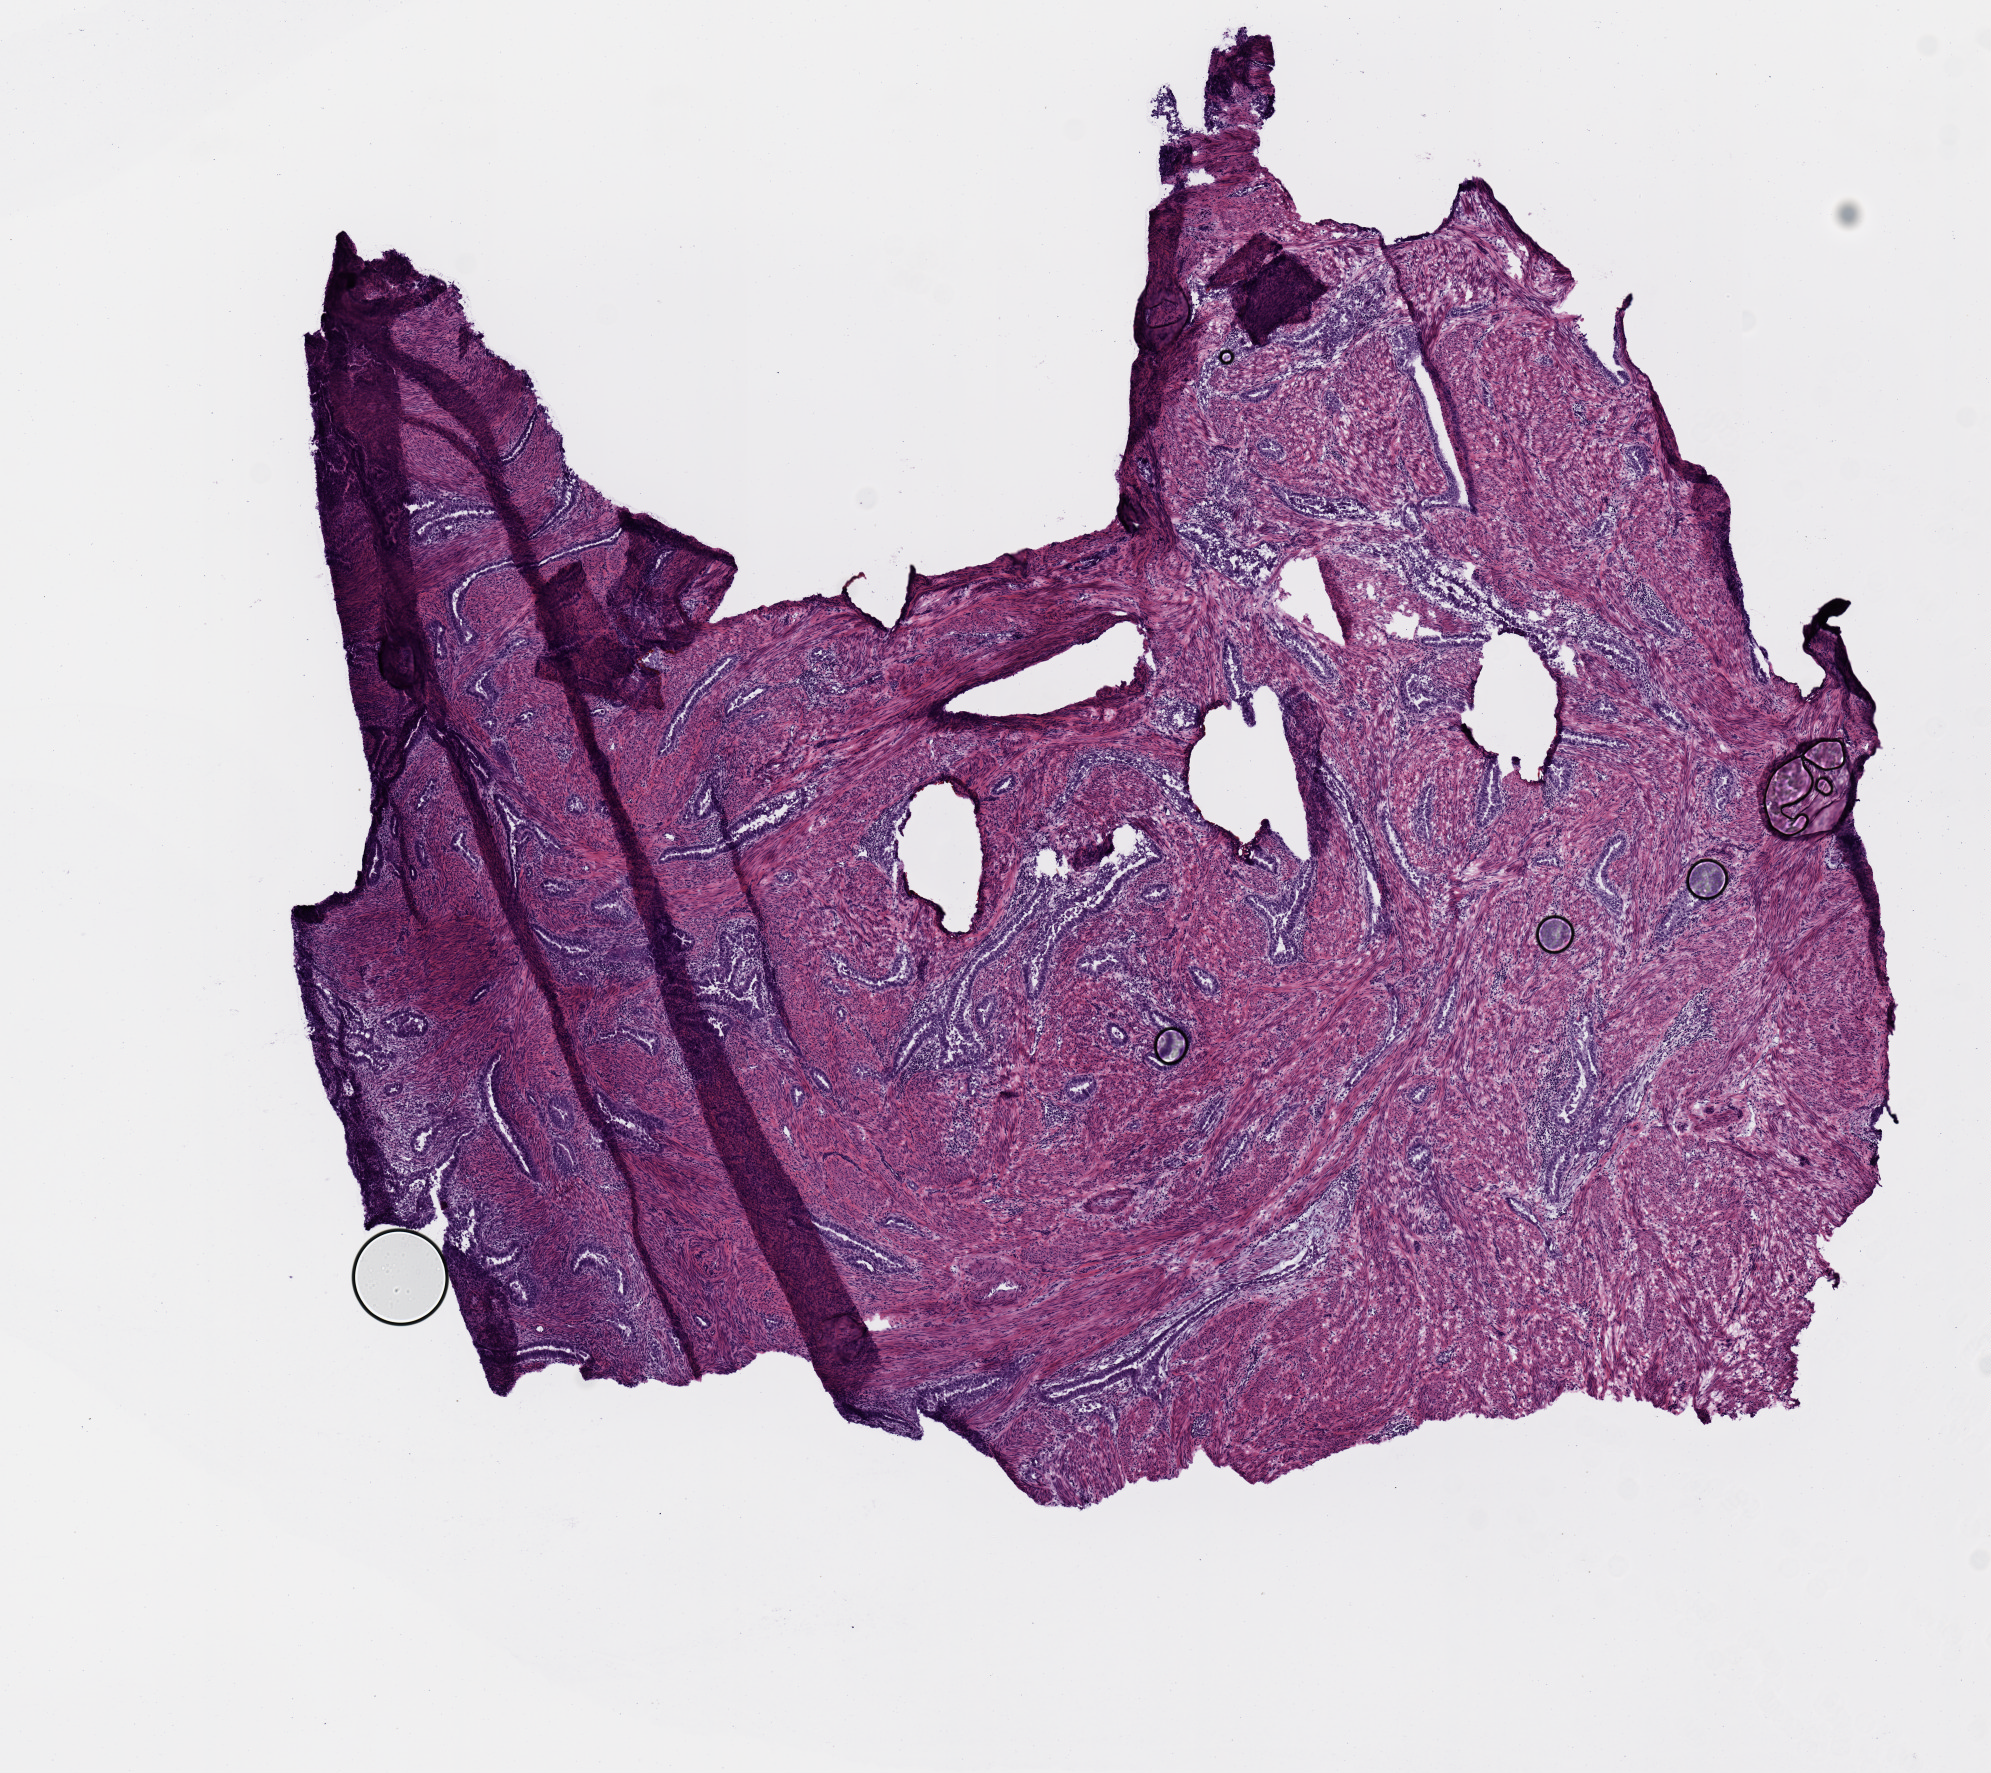
Whole-slide histology image, H&E-stained — shown as a low-resolution overview of the whole scanned area (about 7.9 x 7.0 mm, slide scanned at 20x); frozen section; primary tumour sample from the uterus. Female, age 60 years at initial diagnosis. Histologic grade: G3 (poorly differentiated). Slide review estimates, as recorded: tumour cells 80%, tumour nuclei 60%, normal cells 0%, stromal cells 20%, necrosis 0%. Infiltration values recorded for this section: lymphocyte infiltration 0%, monocyte infiltration 0%, neutrophil infiltration 0%.
FIGO stage: IIIC. Pathologic diagnosis: Serous cystadenocarcinoma, NOS (endometrium). Lymph nodes positive (case pathology): 0 of 9 examined.